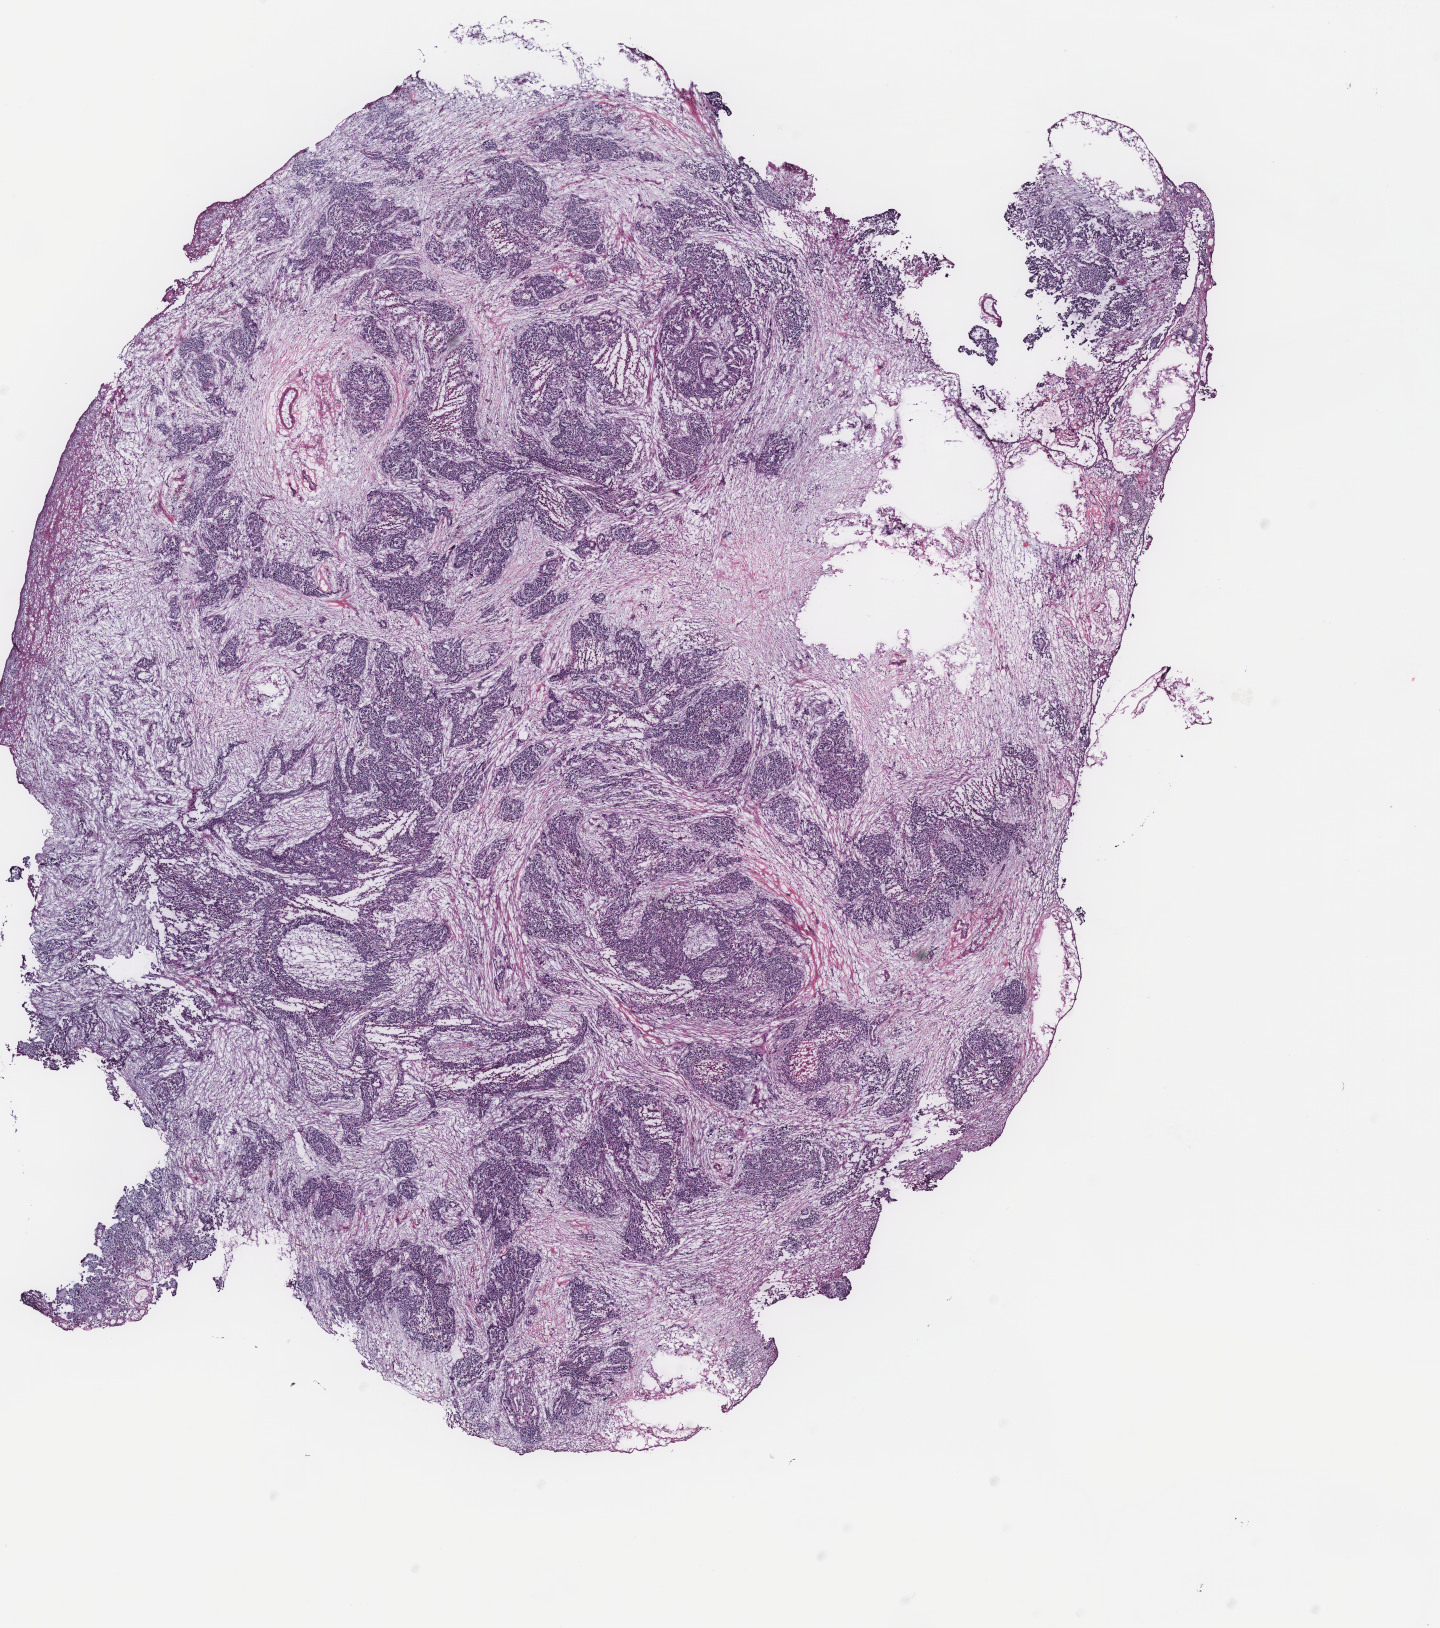
Whole-slide histology image, H&E, a low-resolution overview of the entire scanned area, about 11.5 x 13.0 mm; ovary, tissue type not recorded. Patient sex: female.
Patient diagnosis: Serous adenocarcinoma, NOS.